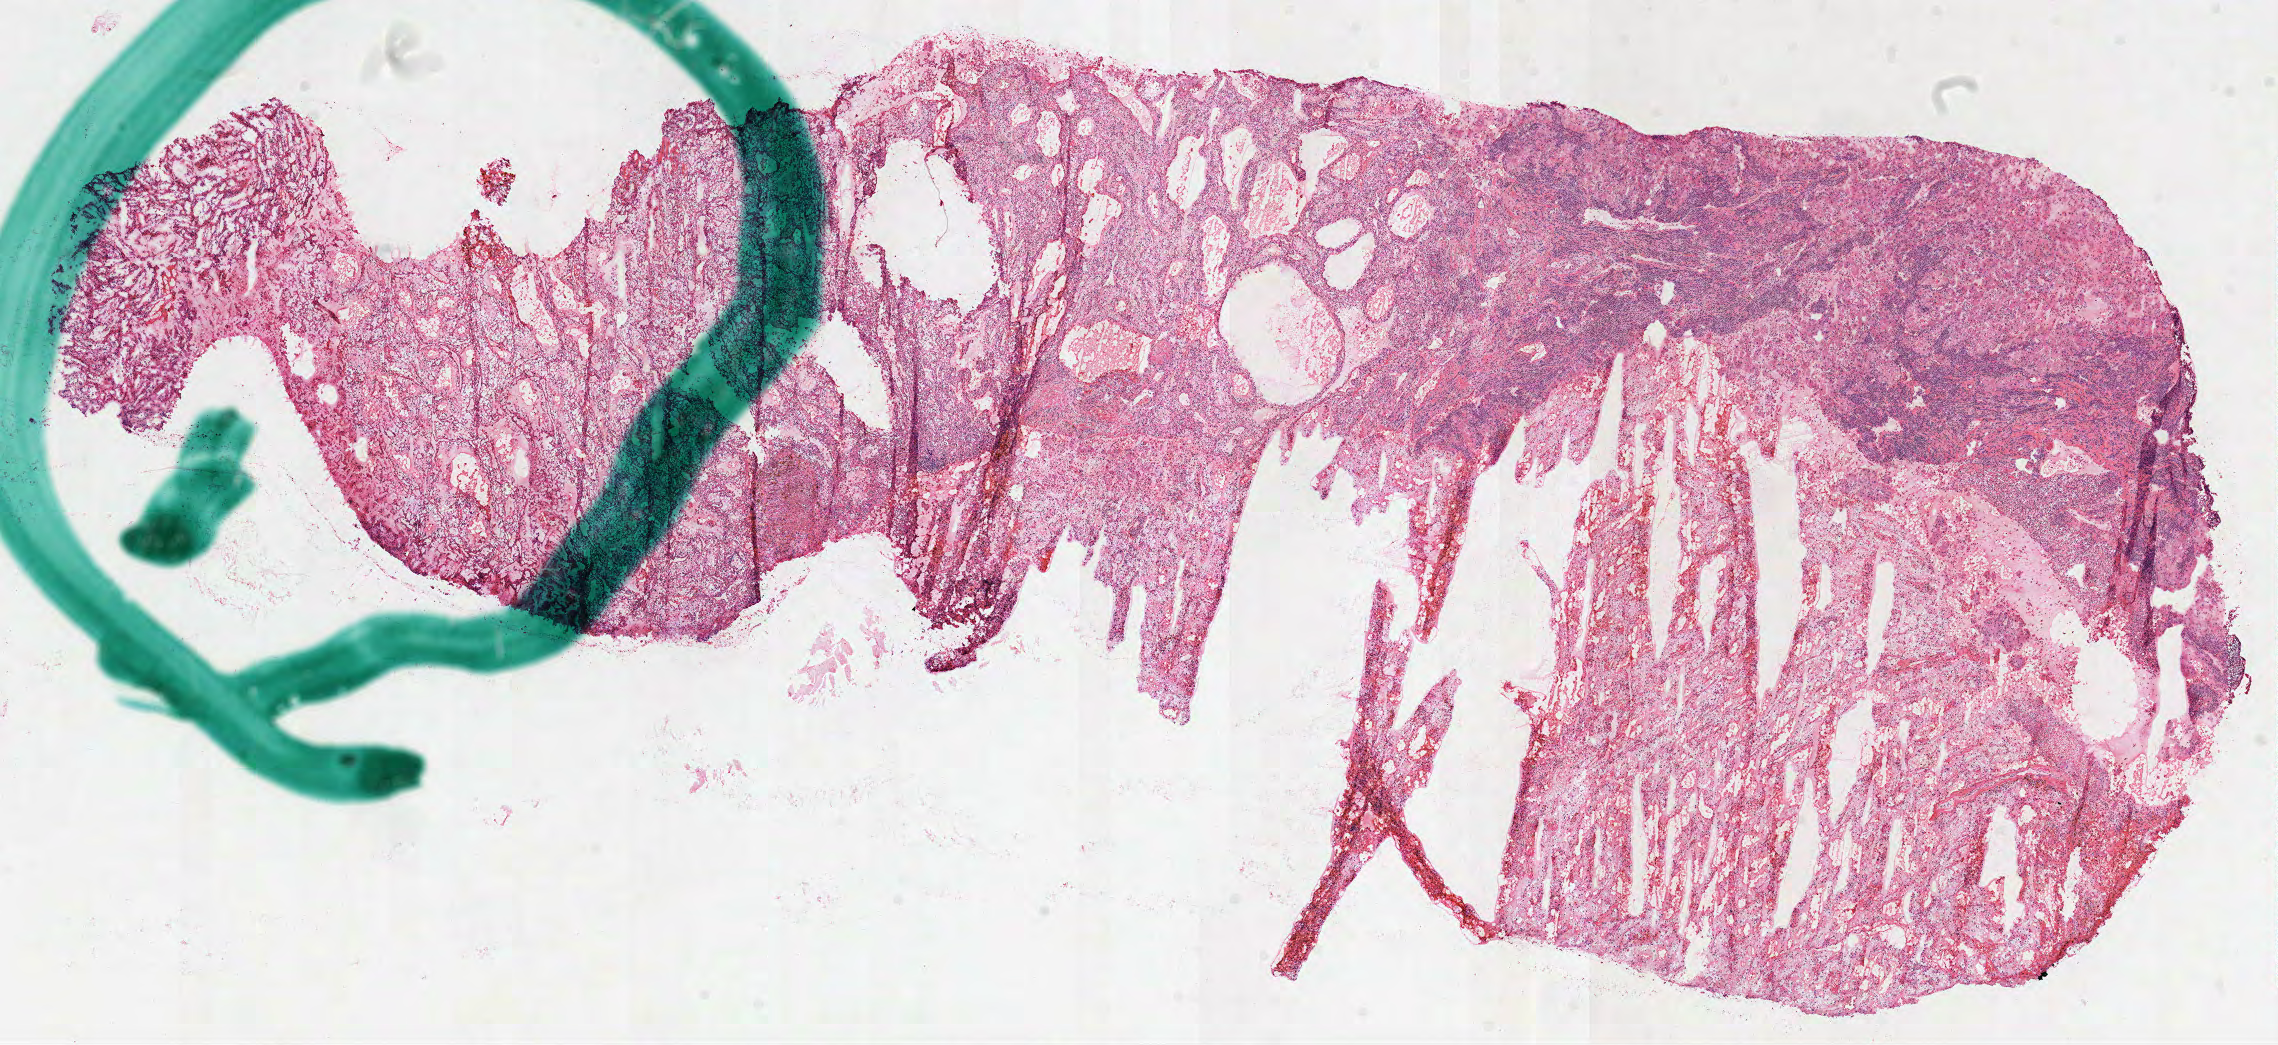
Digitized H&E-stained tissue section (whole slide), shown as a low-resolution overview of the whole scanned area (about 18.4 x 8.4 mm, from a 40x scan), frozen section, sample: primary tumour, kidney. Patient: male, age at initial diagnosis 58 years. Histologic grade: G4 (undifferentiated). Slide review estimates, as recorded: tumour cells 80%, tumour nuclei 65%, normal cells 0%, stromal cells 20%, necrosis 0%. Infiltration values recorded for this section: lymphocyte infiltration 25%, monocyte infiltration 3%, neutrophil infiltration 1%.
• histologic diagnosis: Clear cell adenocarcinoma, NOS
• TNM: T3a NX M1
• AJCC pathologic stage: IV (7th edition)